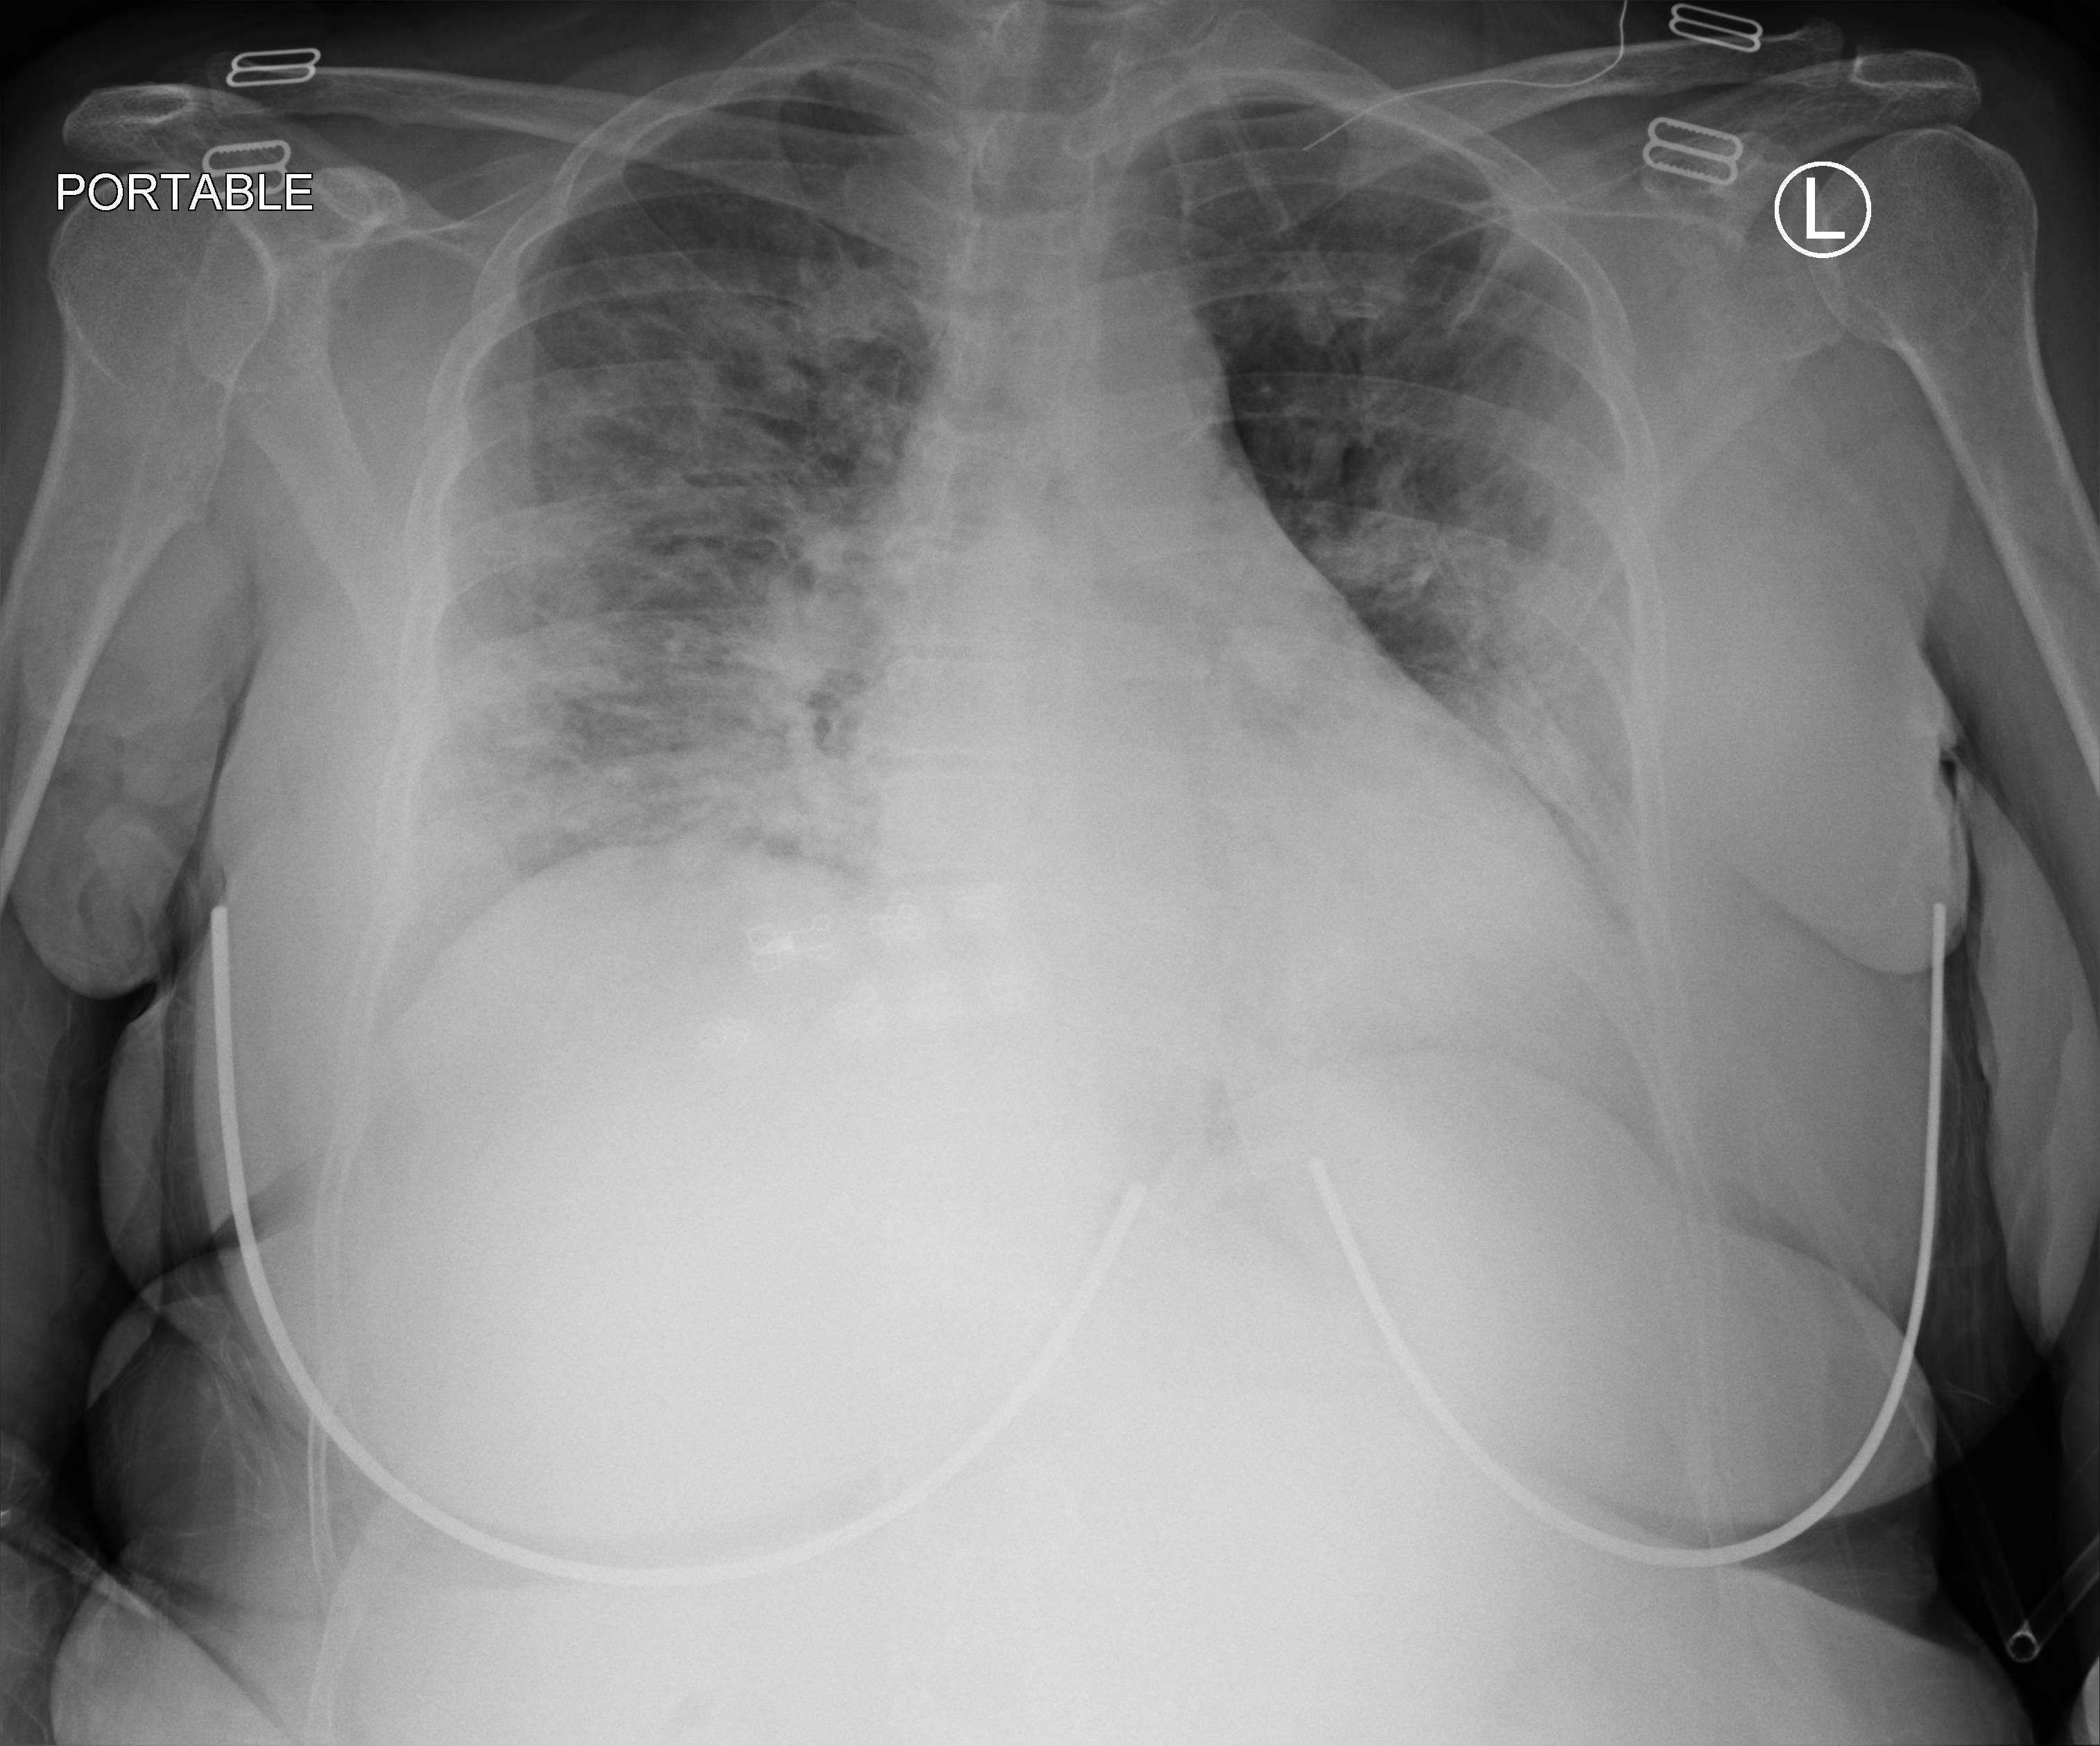
Chest X-ray (portable). Patient hospitalised with COVID-19; female, aged 60–74 years.
Admission-level facts for this patient (not findings on this image; timing relative to this image not recorded): diabetes (admission record): no.